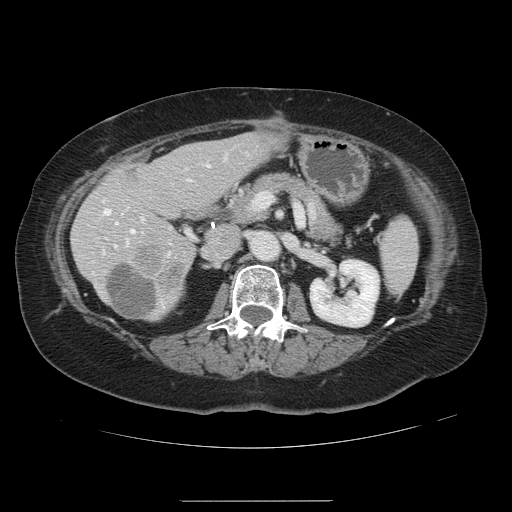
Contrast-enhanced abdominal CT, one axial slice; slice 59 of 141 in the series (ordered by position); 120 kVp; intravenous contrast given; soft-tissue window (W 400 / L 40 HU); 2.5 mm slice thickness; 512 × 512 image matrix, field of view 393 × 393 mm. Female patient, age 74 years. From the clinical record (not read from this slice): diagnosis: colorectal cancer liver metastases, imaged before liver resection; multiple liver metastases: yes.
Outlined on this slice (outlined manually by an expert reader):
- hepatic veins: bounding box (x1, y1, x2, y2) in pixels: (103, 209, 134, 244)
- liver: (72, 135, 274, 321)
- planned liver remnant (the part of the liver to remain after resection): (73, 135, 274, 319)
- portal vein (with intrahepatic branches): (114, 155, 226, 255)
- liver metastasis: (109, 264, 159, 319)
- liver metastasis: (132, 244, 189, 290)